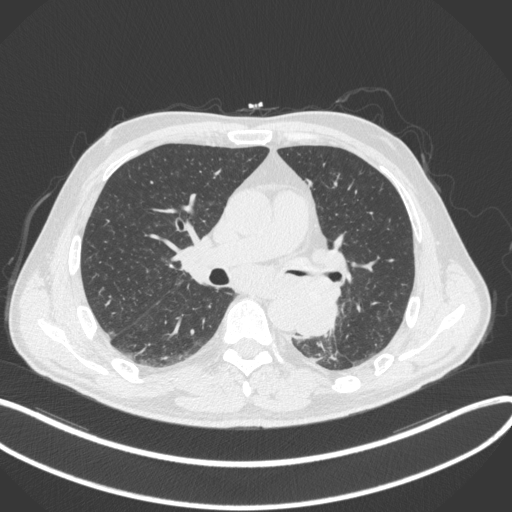
Chest CT, one axial slice. Slice 193 of 328 in the series (ordered by position). 120 kVp. Lung window (W 1500 / L -600 HU). 512 × 512 image matrix. Patient: male, 59 years. Case-level facts recorded for this patient, not image findings: clinical TNM (as recorded): T2a N2 M0.
Outlined on this slice (rectangle marked by the reading radiologist):
- lung tumour (recorded histology: squamous cell carcinoma): bounding box <287,285,340,337> (left, top, right, bottom; pixels)